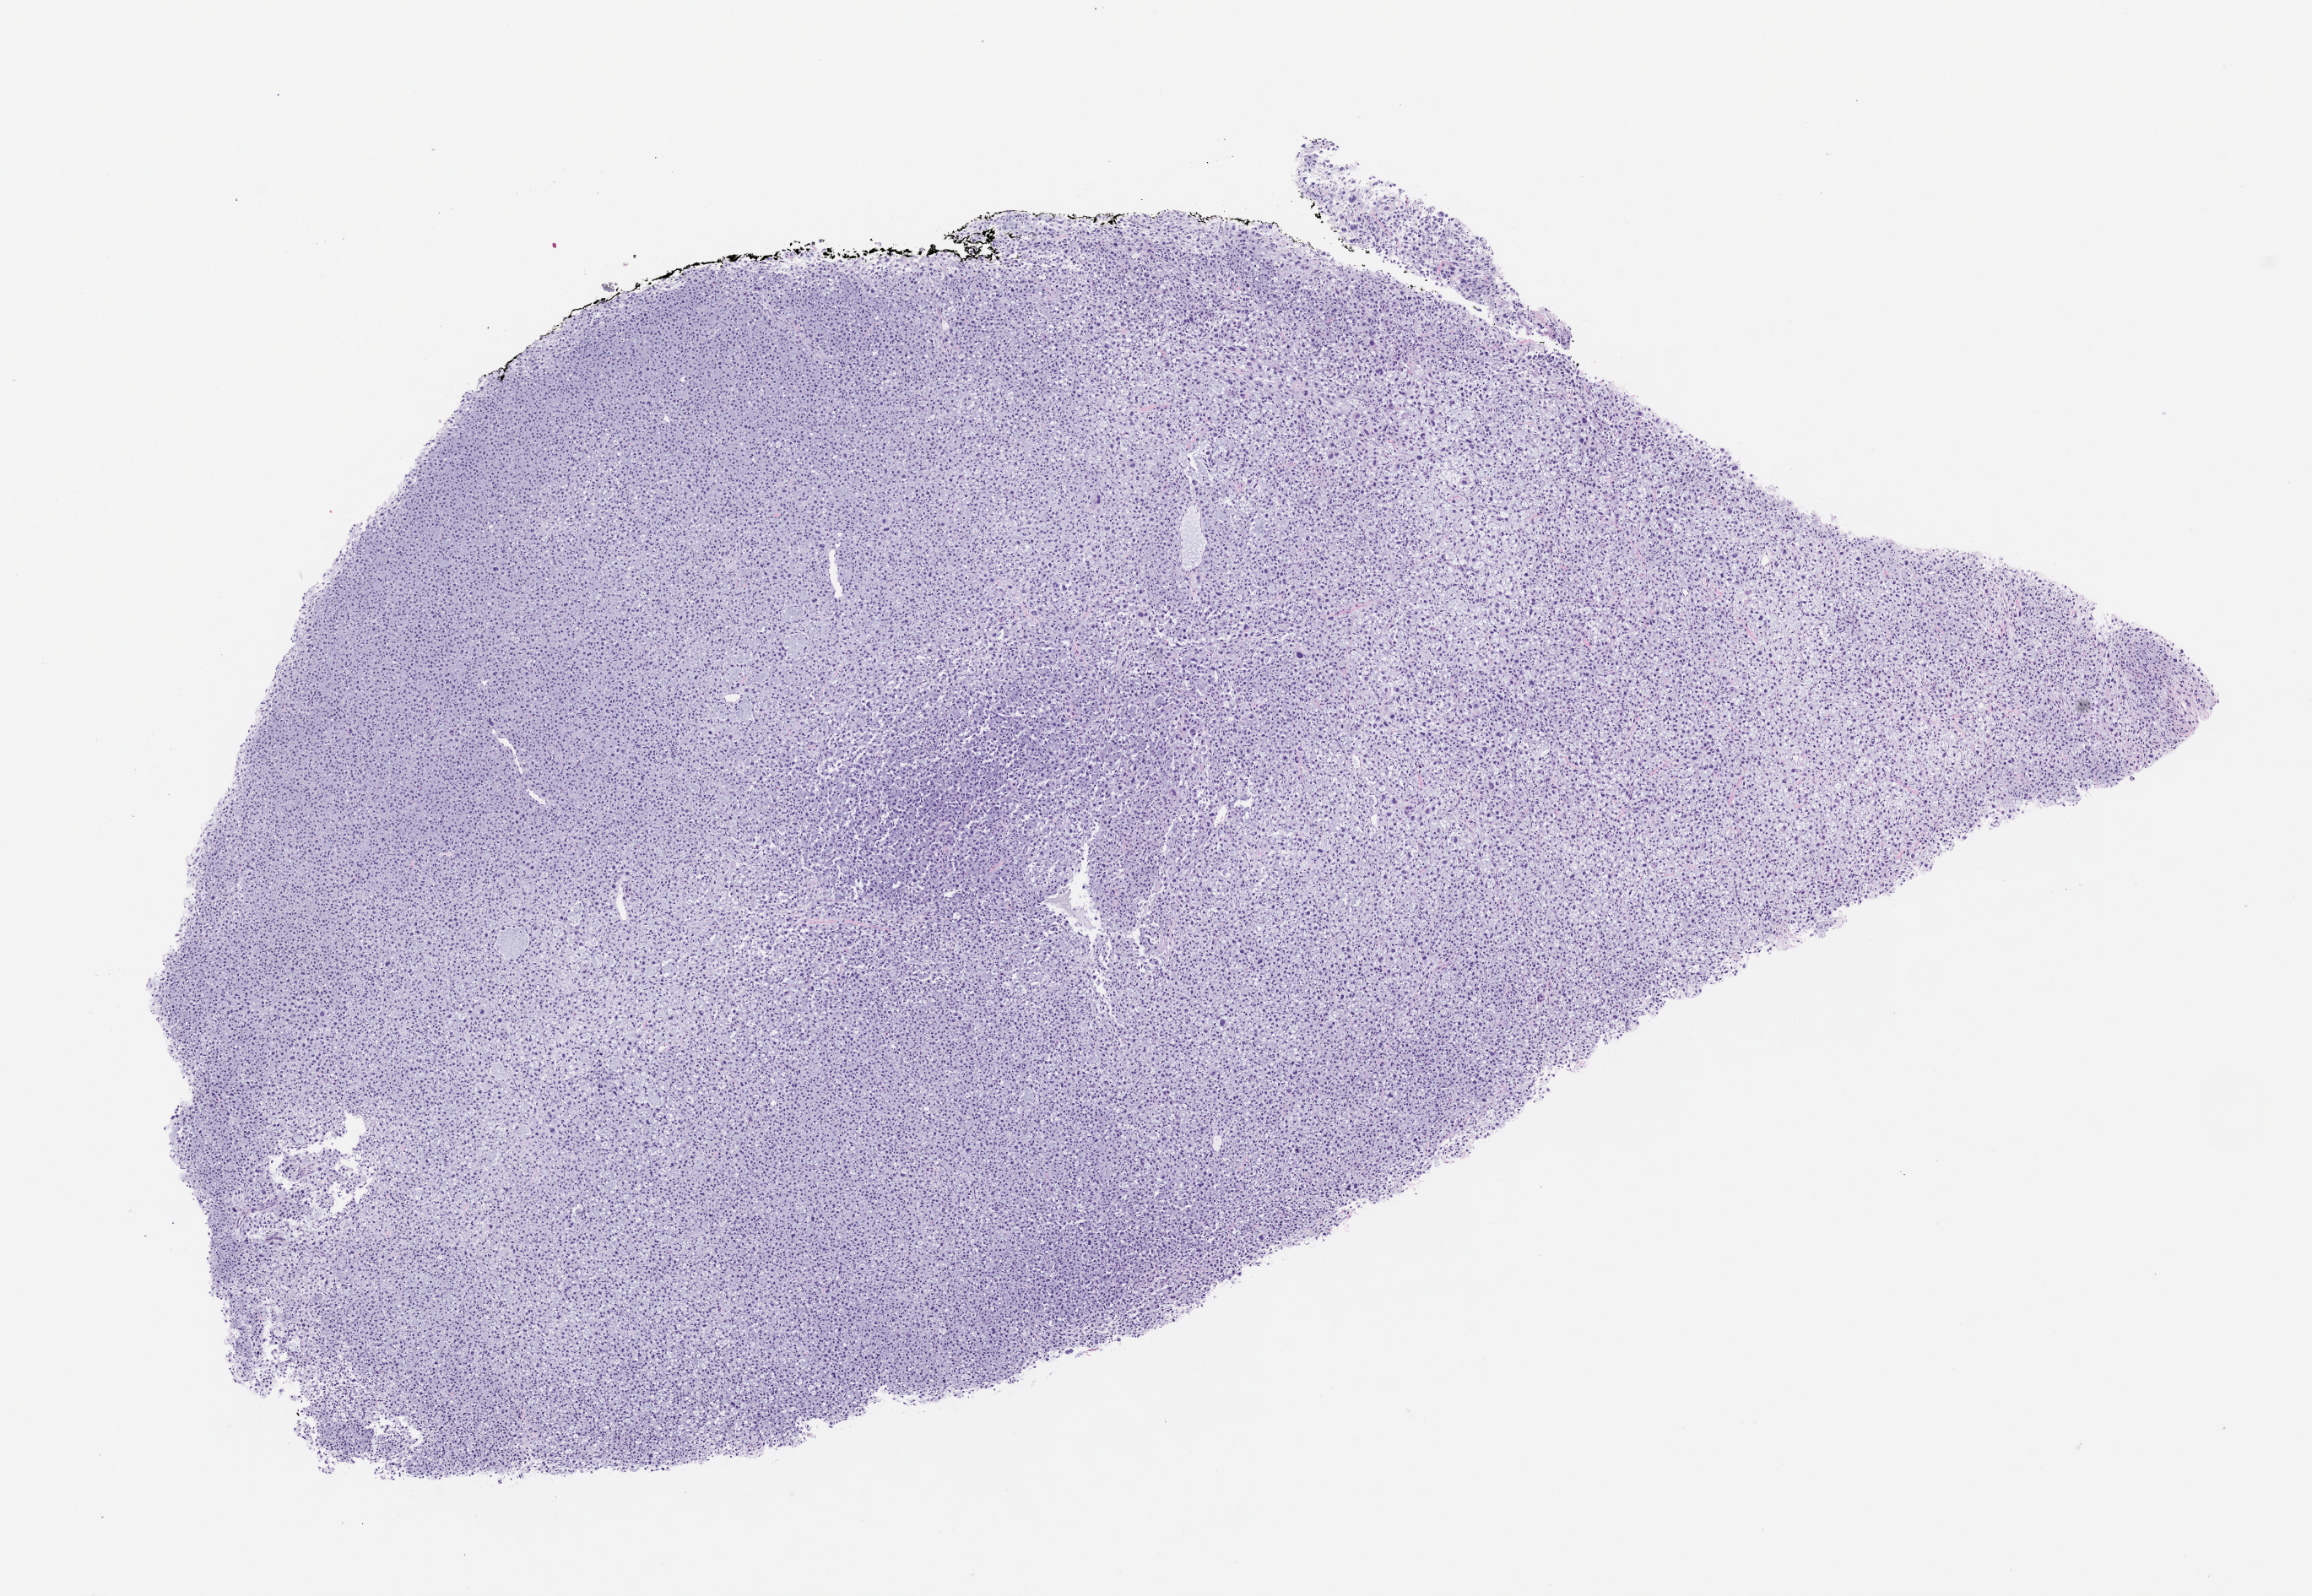
Whole-slide image, haematoxylin and eosin: patient-derived xenograft (human tumor grown in a mouse), passage 1 — whole scanned area (about 11.0 x 7.6 mm) shown as a low-resolution overview, FFPE section, originating tumor site category: musculoskeletal.
Originating patient diagnosis: Myxofibrosarcoma.